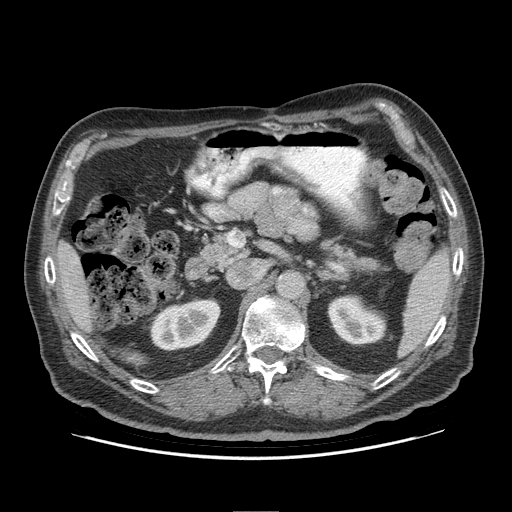
Contrast-enhanced abdominal CT (liver protocol), one axial slice; position 48 of 95 along the scan axis; reconstruction kernel STANDARD; 140 kVp; soft-tissue window (W 400 / L 40 HU); 2.5 mm slice thickness; 512 × 512 image matrix, field of view 400 × 400 mm. From the clinical record (not read from this slice): diagnosis: hepatocellular carcinoma (patient treated with transarterial chemoembolisation; whether this scan precedes or follows treatment is not stated here); TNM stage (as recorded): Stage-IVB; Child-Pugh class: A; tumour differentiation: well differentiated; tumour nodularity: uninodular.
Structures marked on this image (semi-automatically segmented with operator editing):
- liver parenchyma outside the tumour (the mass and vessels are separate outlines, so this box may not span the whole liver): bounding box [x1, y1, x2, y2] px = [56, 241, 92, 332]